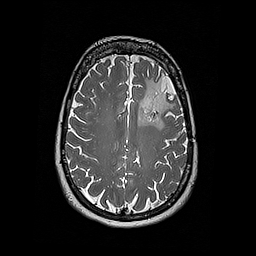
Brain MRI from a brain-tumour surgery series, one axial slice; slice 126 of 192 in the series (ordered by position); 1 mm slice thickness; 256 × 256 image matrix. From the clinical record (not read from this slice): histopathology: Oligodendroglioma; WHO grade: 2; IDH mutation: yes; tumour location: Left Frontal.
Outlined on this slice (expert manual segmentation):
- tumour: bounding box <137,78,164,130> (left, top, right, bottom; pixels)